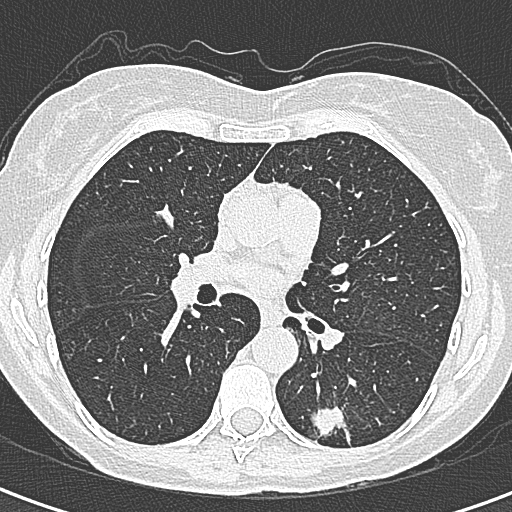
Low-dose screening chest CT, axial slice, first (baseline) screen, lung window (W 1500 / L -600 HU), 1 mm slice thickness, slice 140 of 328 in the series. Female, age 58 years at enrolment.
Expert reader's lesion annotation, bounding box <299,386,368,456> (left, top, right, bottom; pixels). The screening reader recorded 2 non-calcified nodules or masses ≥4 mm on this exam (left lower lobe, right lower lobe); which of them this box marks is not recorded. Official screen result: positive, change unspecified: nodule(s) >= 4 mm or enlarging nodule(s), mass(es), or other non-specific abnormalities suspicious for lung cancer. Later outcome: lung cancer diagnosed 22 days after this screen — adenocarcinoma, NOS, left lower lobe, moderately differentiated (G2), stage IA (AJCC 6th edition), 25 mm at pathology.